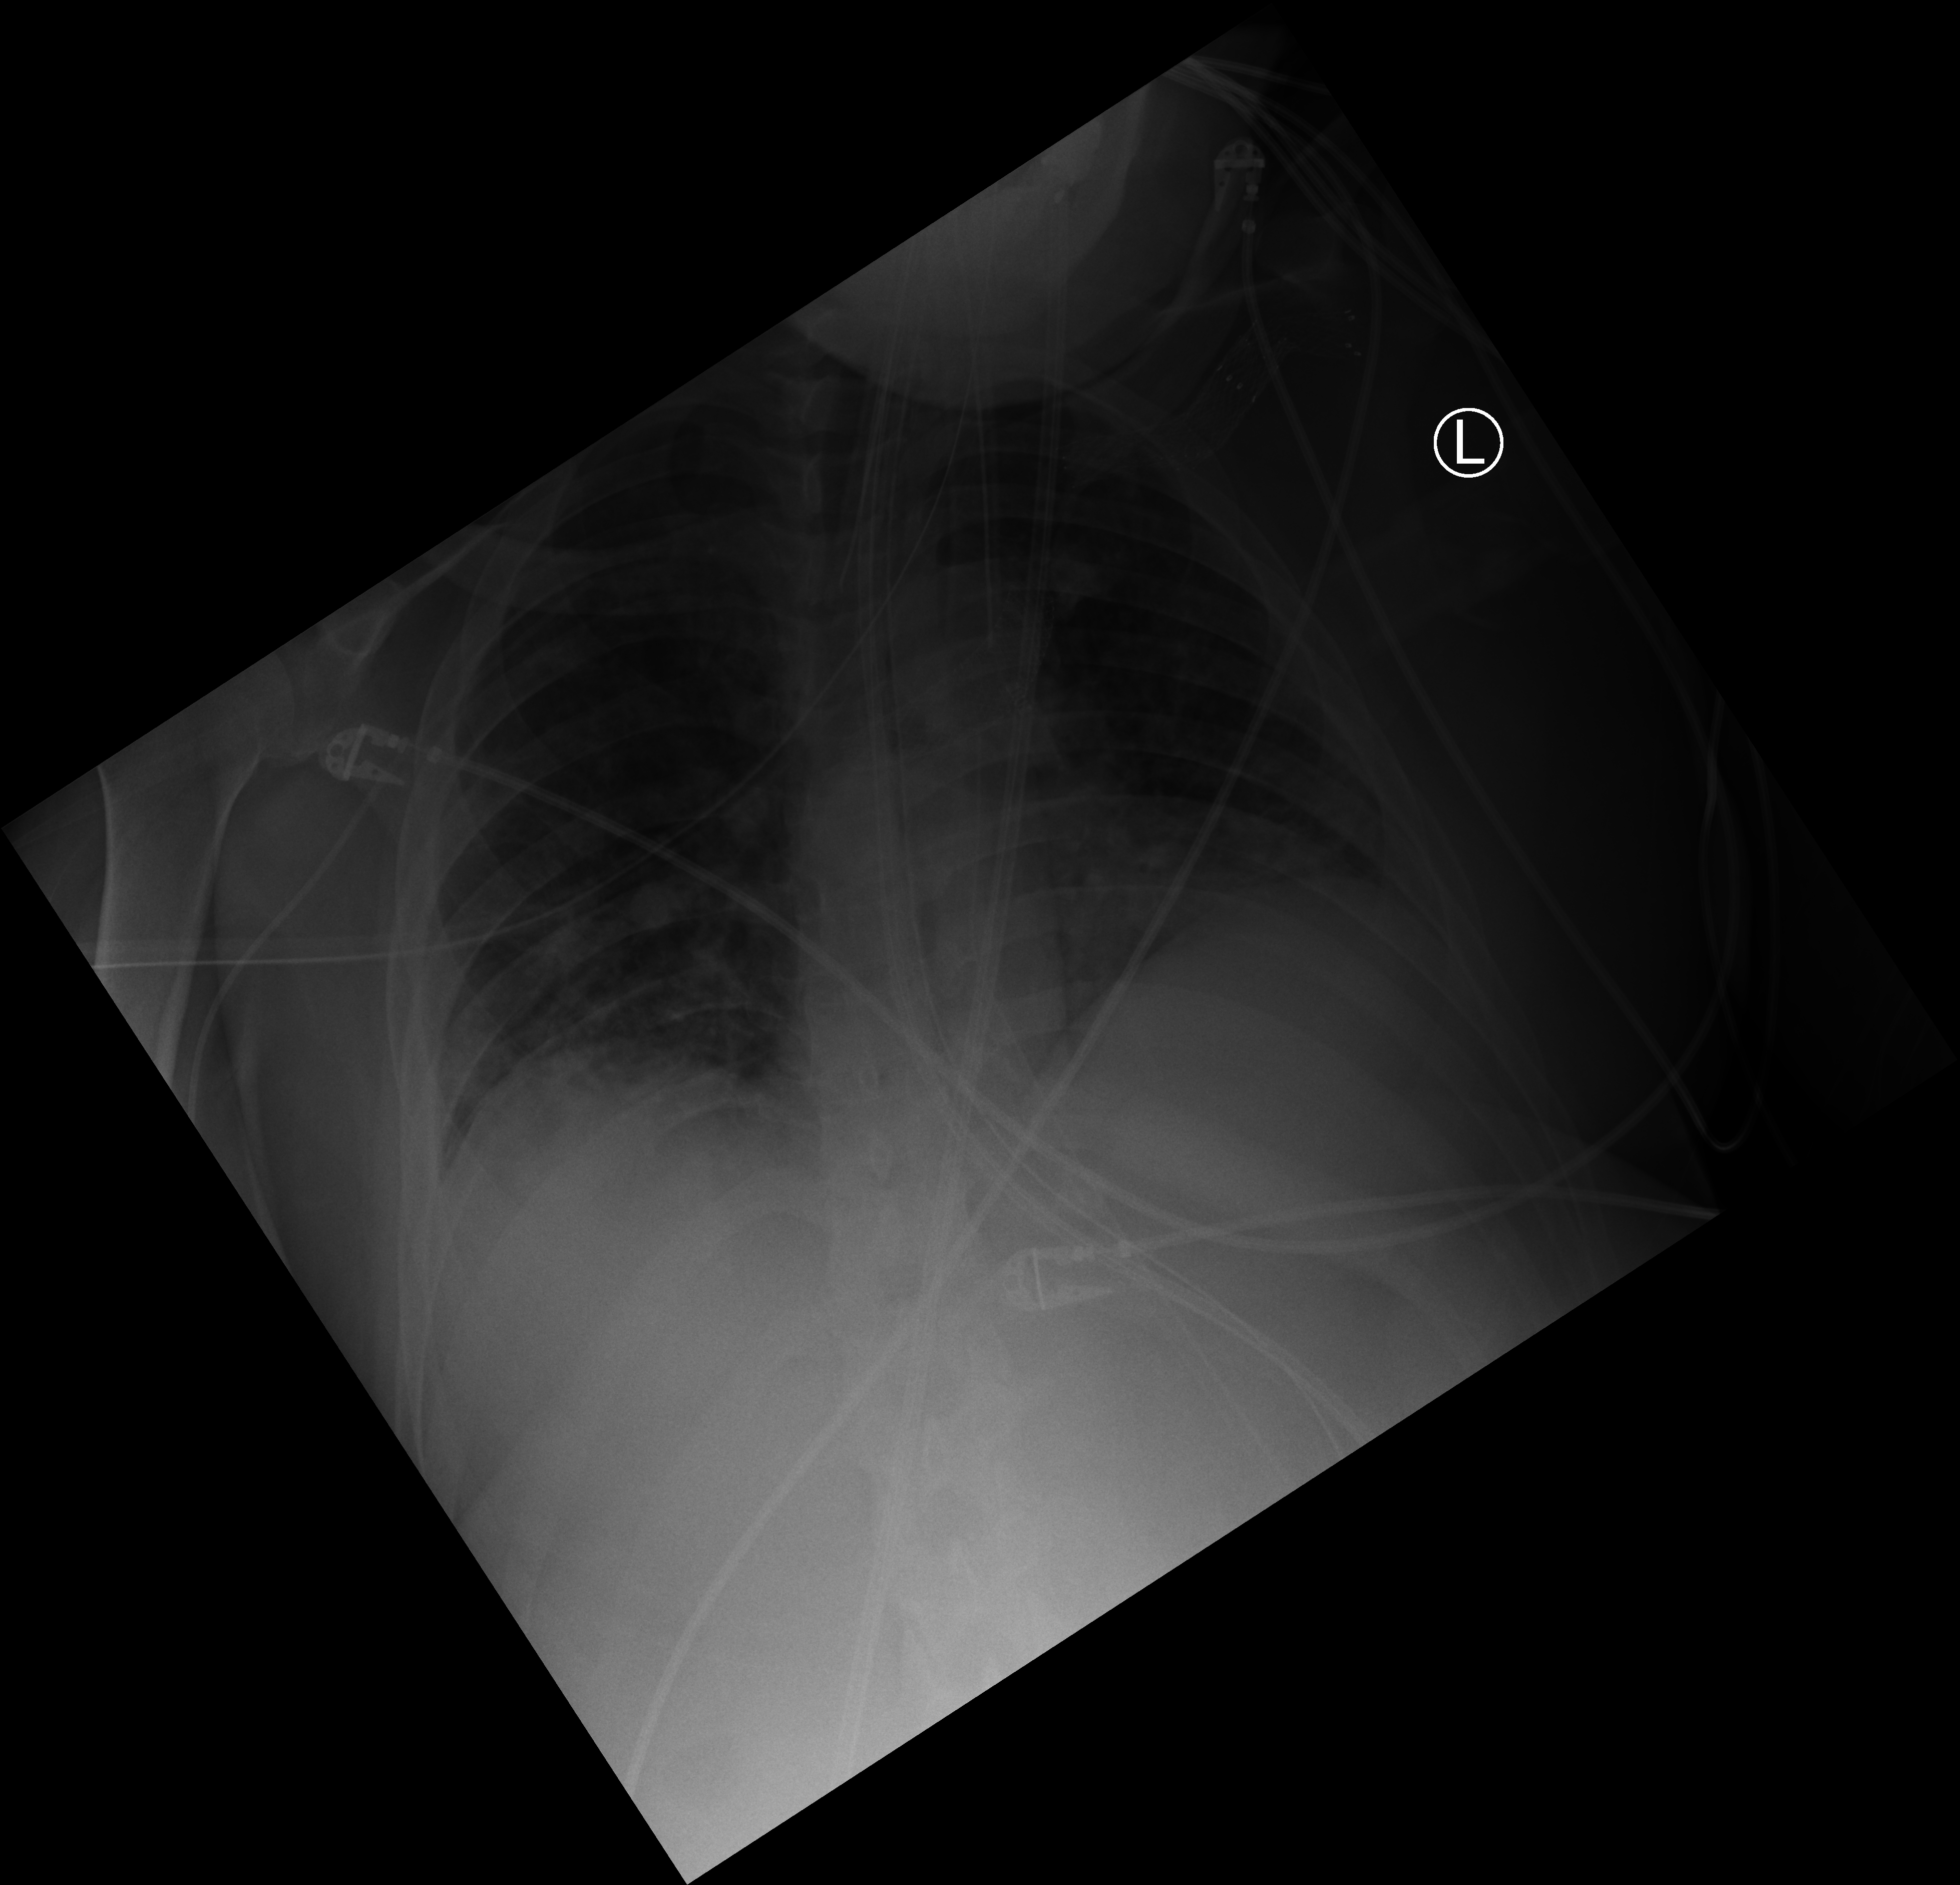
Bedside chest radiograph (computed radiography), anteroposterior (AP) projection. Patient hospitalised with COVID-19; male, aged 18–59 years.
Admission-level facts for this patient (not findings on this image; timing relative to this image not recorded): admitted to intensive care during this hospital stay: yes; length of hospital stay: 41 days; mechanically ventilated during this hospital stay: yes.